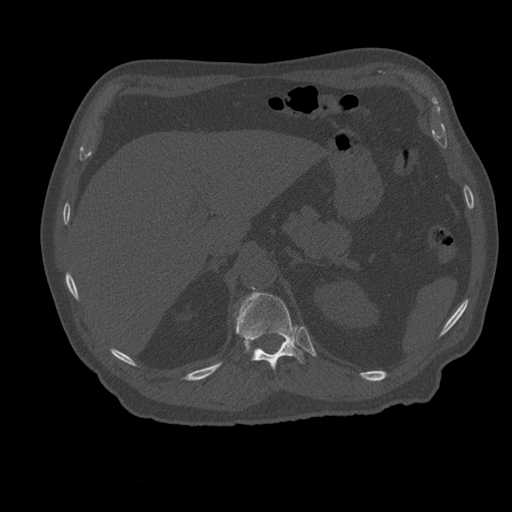
CT including the spine, one axial slice. Position 260 of 399 along the scan axis. Reconstruction kernel STANDARD. Bone window (W 1800 / L 400 HU). 512 × 512 image matrix, field of view 407 × 407 mm. Patient age 73 years. Case-level facts recorded for this patient, not image findings: primary cancer: prostate; vertebrae with lytic lesions (as recorded): L2.
Outlined on this slice (semi-automatic segmentation, software-assisted and operator-edited):
- T12 vertebra: box from (x=236, y=293) to (x=304, y=370) px